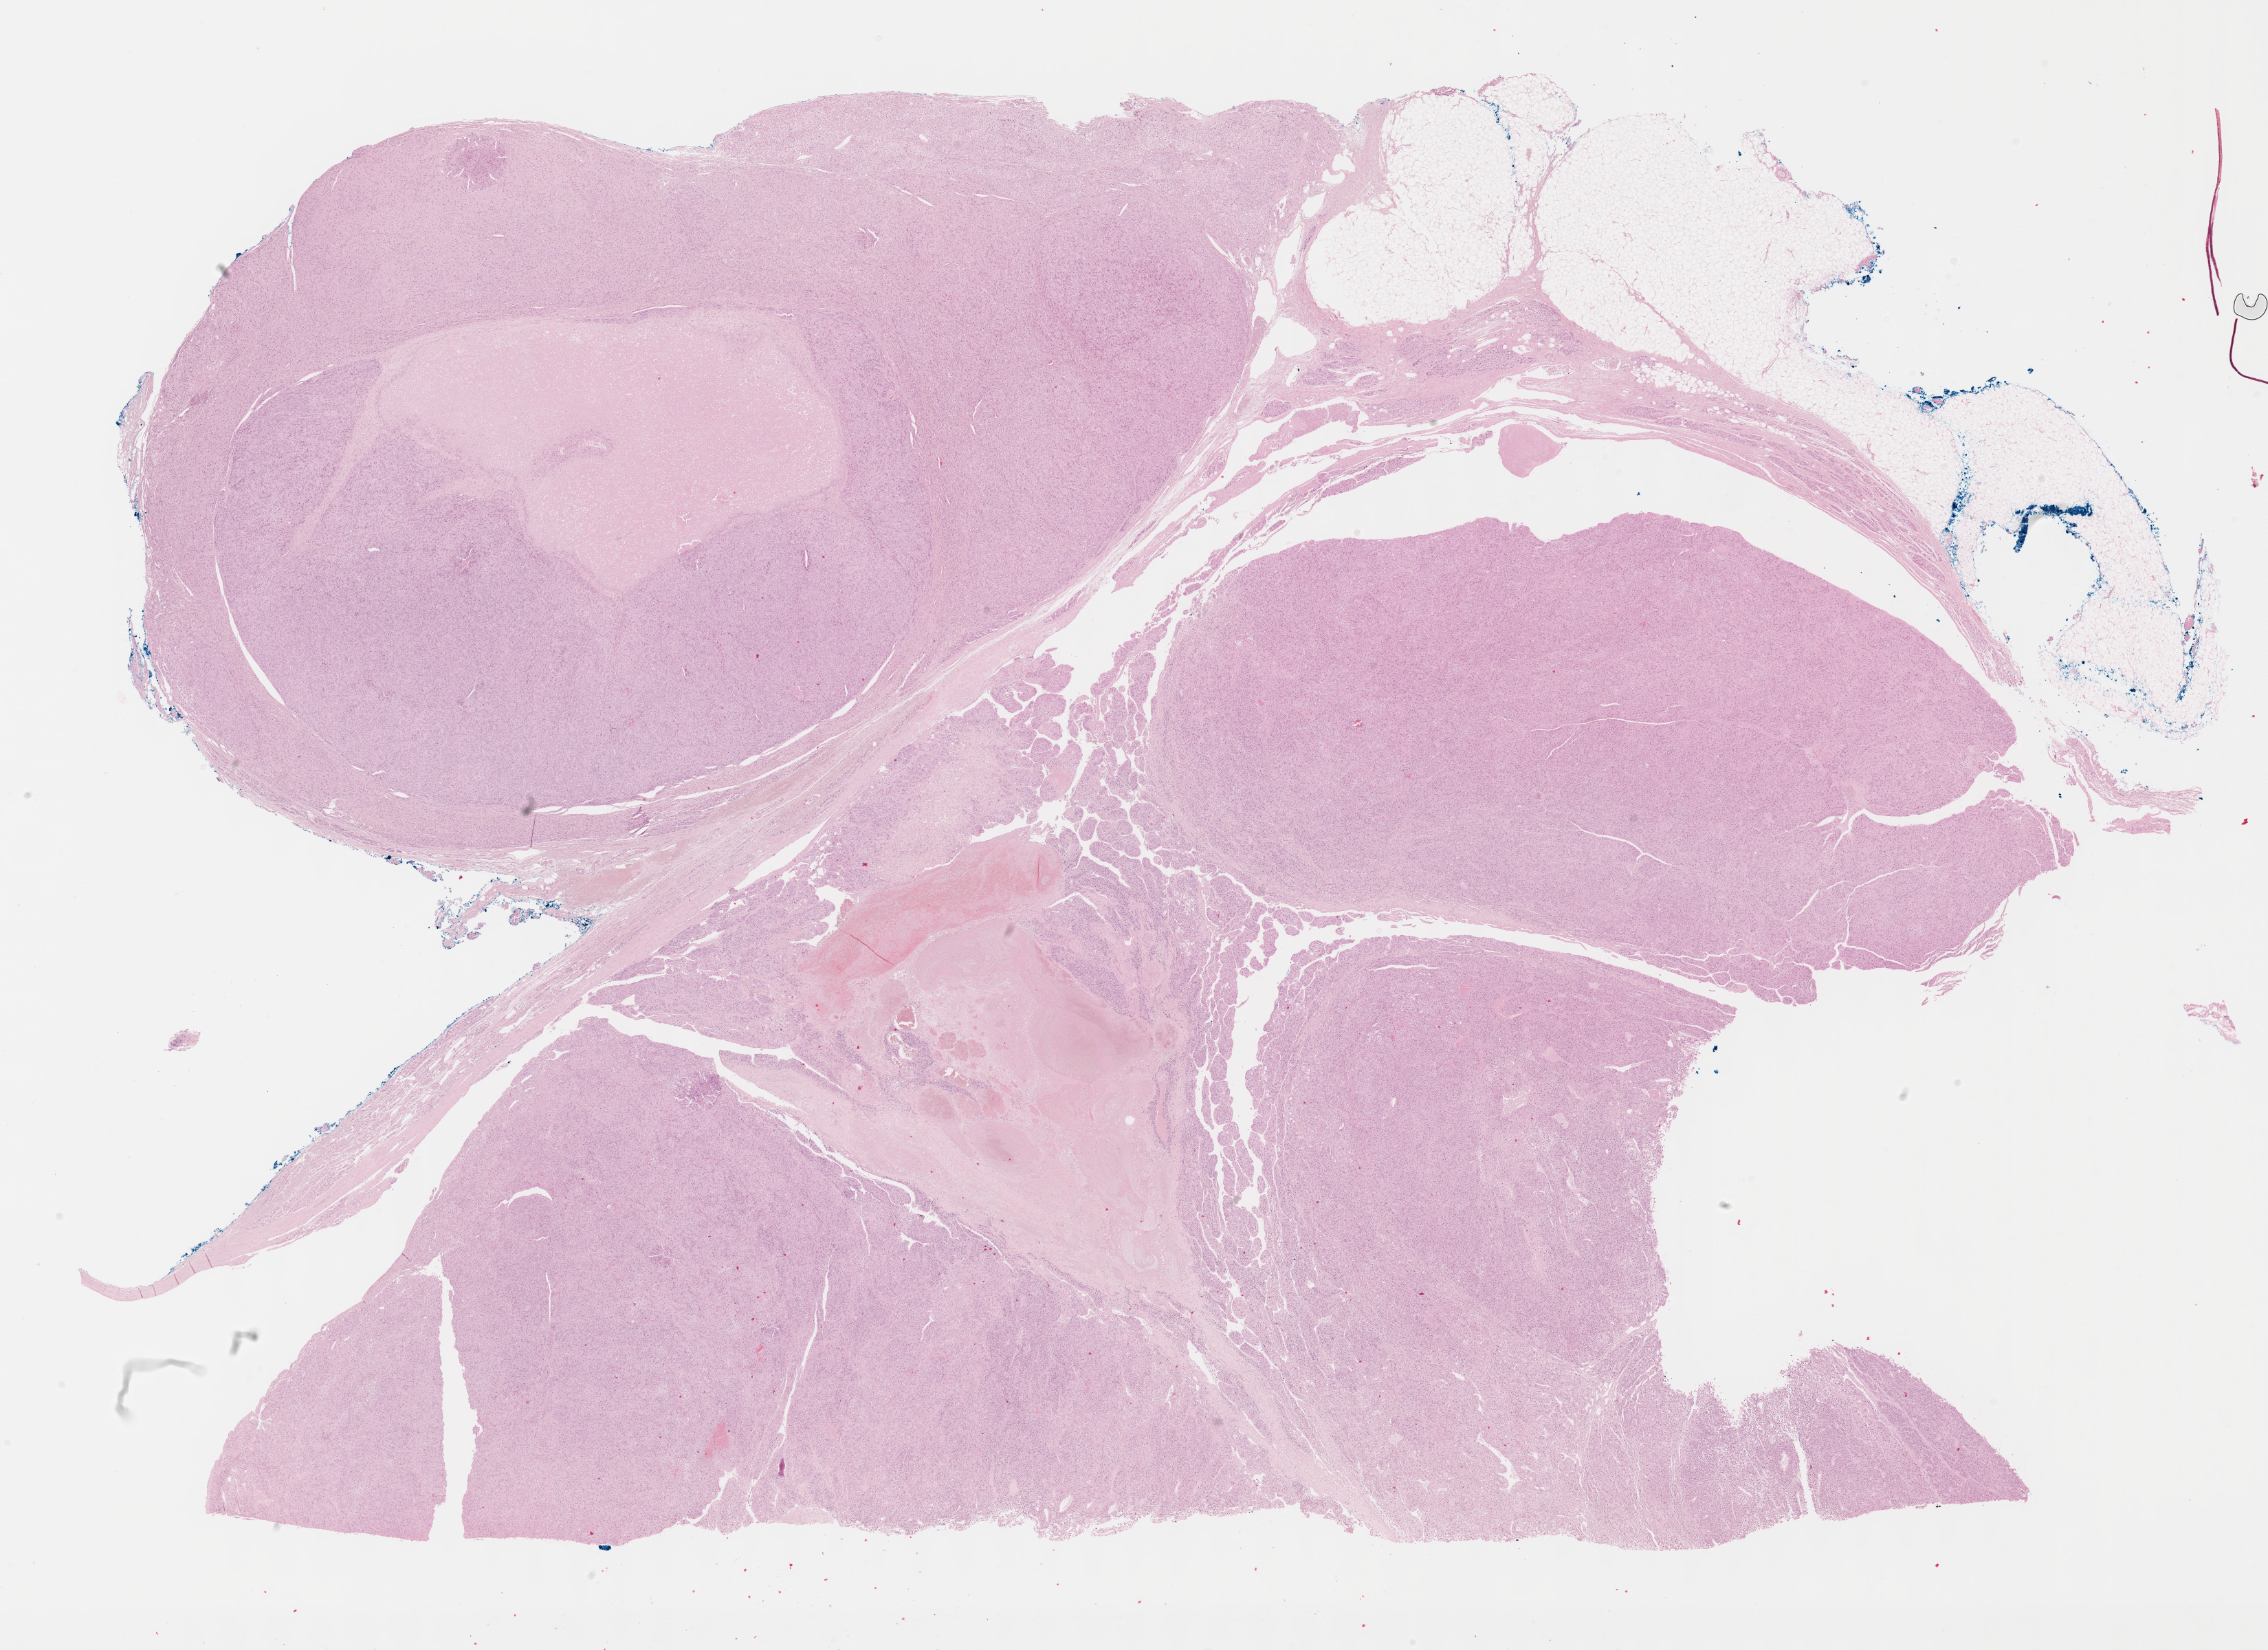
H&E whole-slide image, whole scanned area (about 26.7 x 19.4 mm, slide scanned at 40x) shown as a low-resolution overview. FFPE section. Adrenal cortex, primary tumour sample. Female, age 17 years at initial diagnosis.
Laterality: left. Histologic diagnosis: Adrenal cortical carcinoma (cortex of adrenal gland).